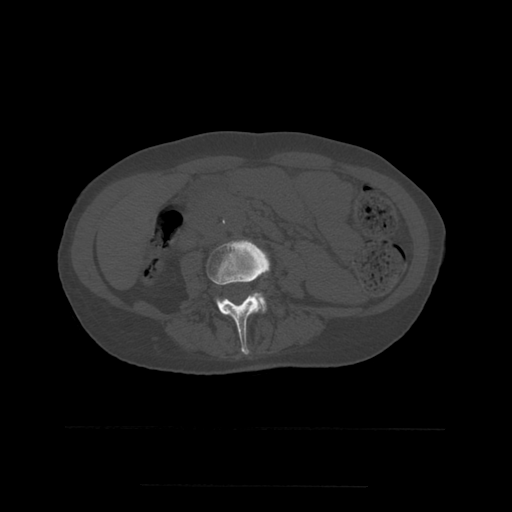
CT including the spine, one axial slice; slice 184 of 544 in the series (ordered by position); bone window (W 1800 / L 400 HU); 512 × 512 image matrix, field of view 350 × 350 mm. Patient age 58 years. From the clinical record (not read from this slice): primary cancer: lung.
Annotated regions visible in this slice (semi-automatic segmentation, software-assisted and operator-edited):
- L3 vertebra: bounding box (x1, y1, x2, y2) in pixels: (206, 240, 270, 355)
- L4 vertebra: (220, 292, 267, 313)